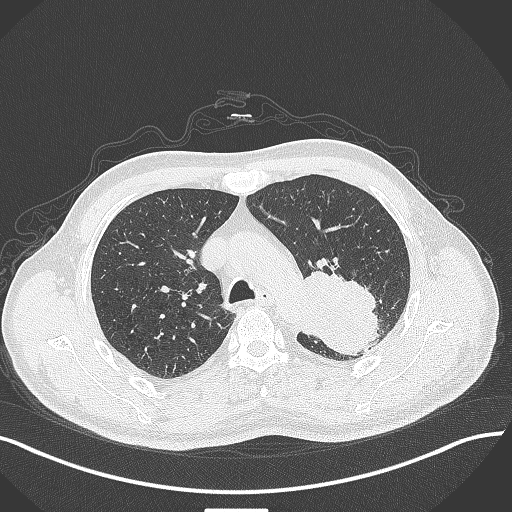
Chest CT, one axial slice. Slice 306 of 429 in the series (ordered by position). Lung window (W 1500 / L -600 HU). 1 mm slice thickness. 512 × 512 image matrix, field of view 400 × 400 mm. Patient: male, 55 years. Case-level facts recorded for this patient, not image findings: clinical TNM (as recorded): T3 N0 M1c; histopathological grade: G3.
Annotated regions visible in this slice (bounding box drawn by a radiologist):
- lung tumour (recorded histology: adenocarcinoma): bounding box <298,268,383,357> (left, top, right, bottom; pixels)